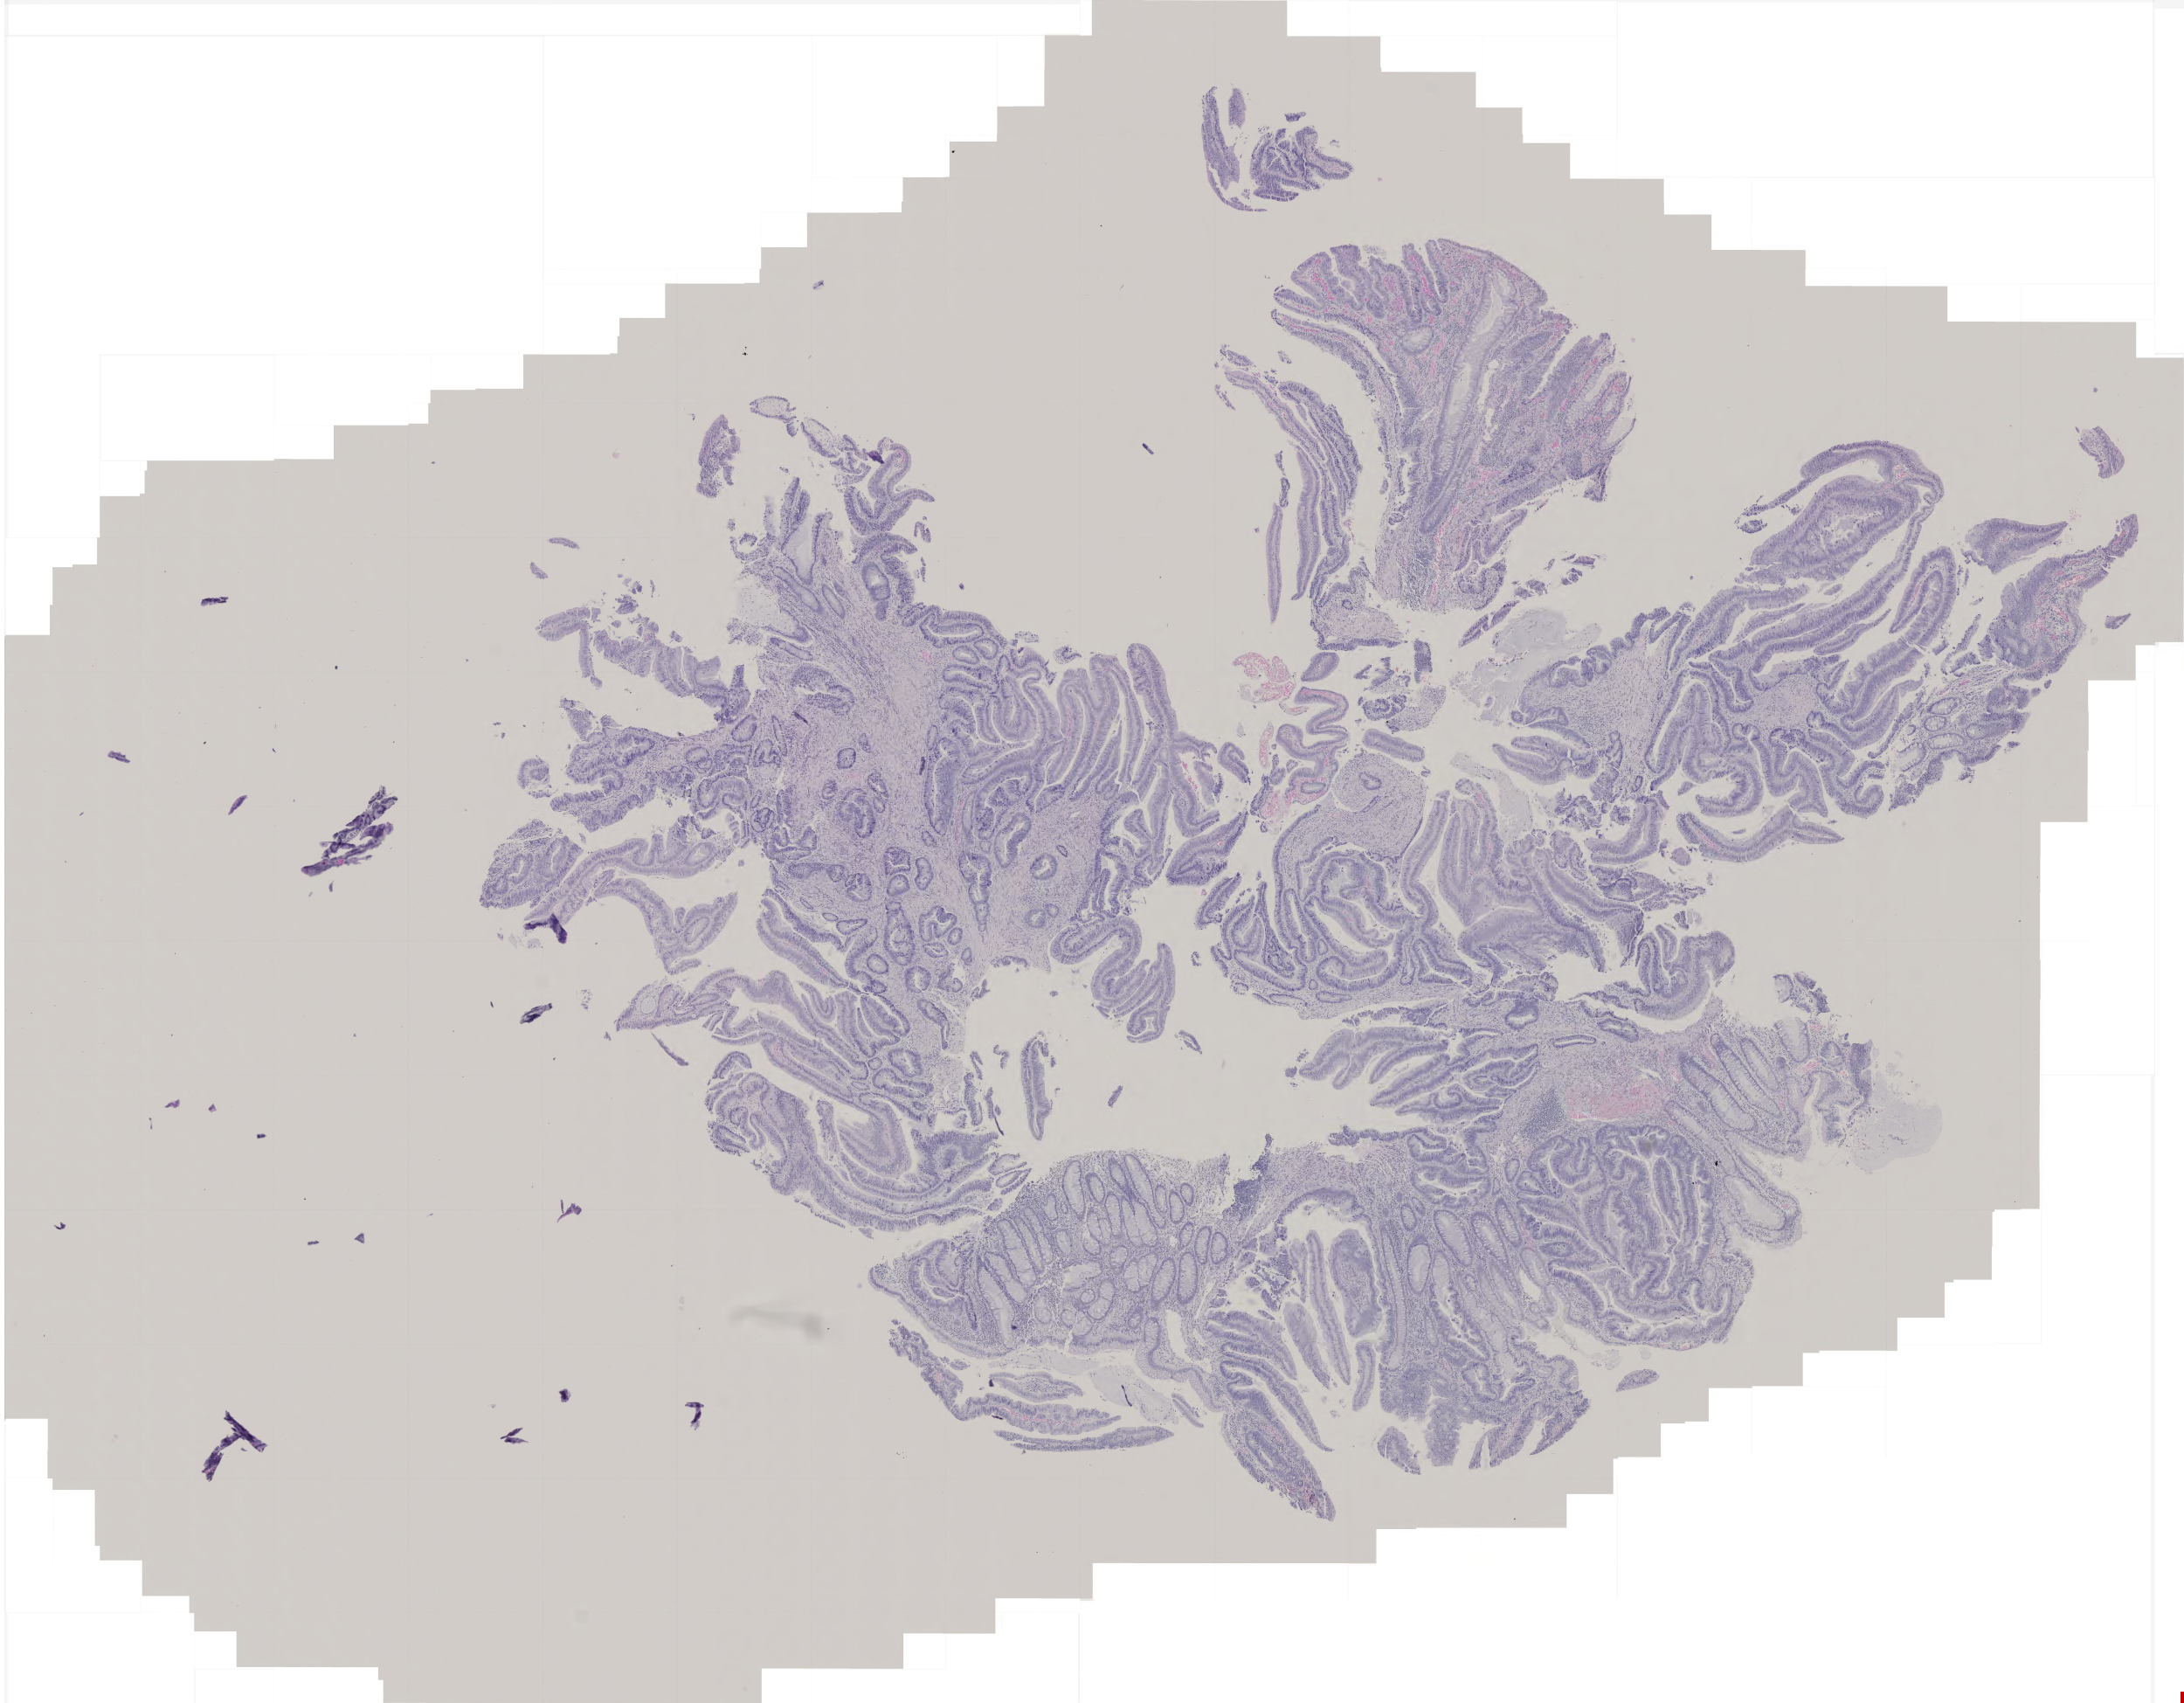
Hematoxylin and eosin (H&E) stained whole-slide image — whole scanned area (about 5.0 x 3.9 mm) shown as a low-resolution overview, formalin-fixed paraffin-embedded (FFPE) diagnostic section, rectum, primary tumour sample. Female patient; age at initial diagnosis 66 years.
Diagnosis: Adenocarcinoma, NOS (rectosigmoid junction).